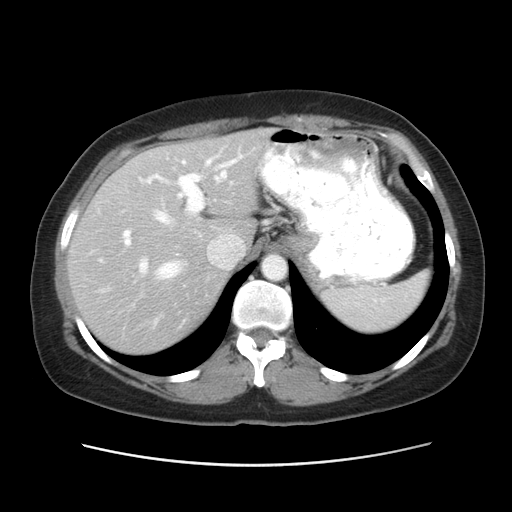
Contrast-enhanced abdominal CT, one axial slice. Slice 38 of 52 in the series (ordered by position). Reconstruction kernel STANDARD. Intravenous contrast given. Soft-tissue window (W 400 / L 40 HU). 5 mm slice thickness. 512 × 512 image matrix, field of view 362 × 362 mm. Female patient, age 48 years. From the clinical record (not read from this slice): diagnosis: colorectal cancer liver metastases, imaged before liver resection; multiple liver metastases: yes; largest metastasis: 4.5 cm.
Structures marked on this image (outlined manually by an expert reader):
- hepatic veins: box from (x=100, y=153) to (x=242, y=278) px
- liver: (x=69, y=131)–(x=267, y=353)
- planned liver remnant (the part of the liver to remain after resection): (x=143, y=131)–(x=267, y=242)
- portal vein (with intrahepatic branches): (x=123, y=159)–(x=212, y=273)